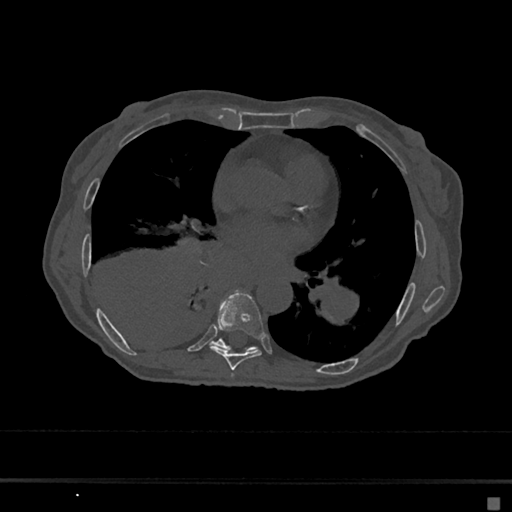
CT including the spine, one axial slice. Reconstruction kernel Br40s/3. Bone window (W 1800 / L 400 HU). 512 × 512 image matrix, field of view 360 × 360 mm. Patient: female, 68 years. From the clinical record (not read from this slice): primary cancer: renal.
Structures marked on this image (semi-automatic segmentation, software-assisted and operator-edited):
- T6 vertebra: bounding box <231,374,234,378> (left, top, right, bottom; pixels)
- T7 vertebra: <209,291,264,371>
- T8 vertebra: <212,339,256,351>